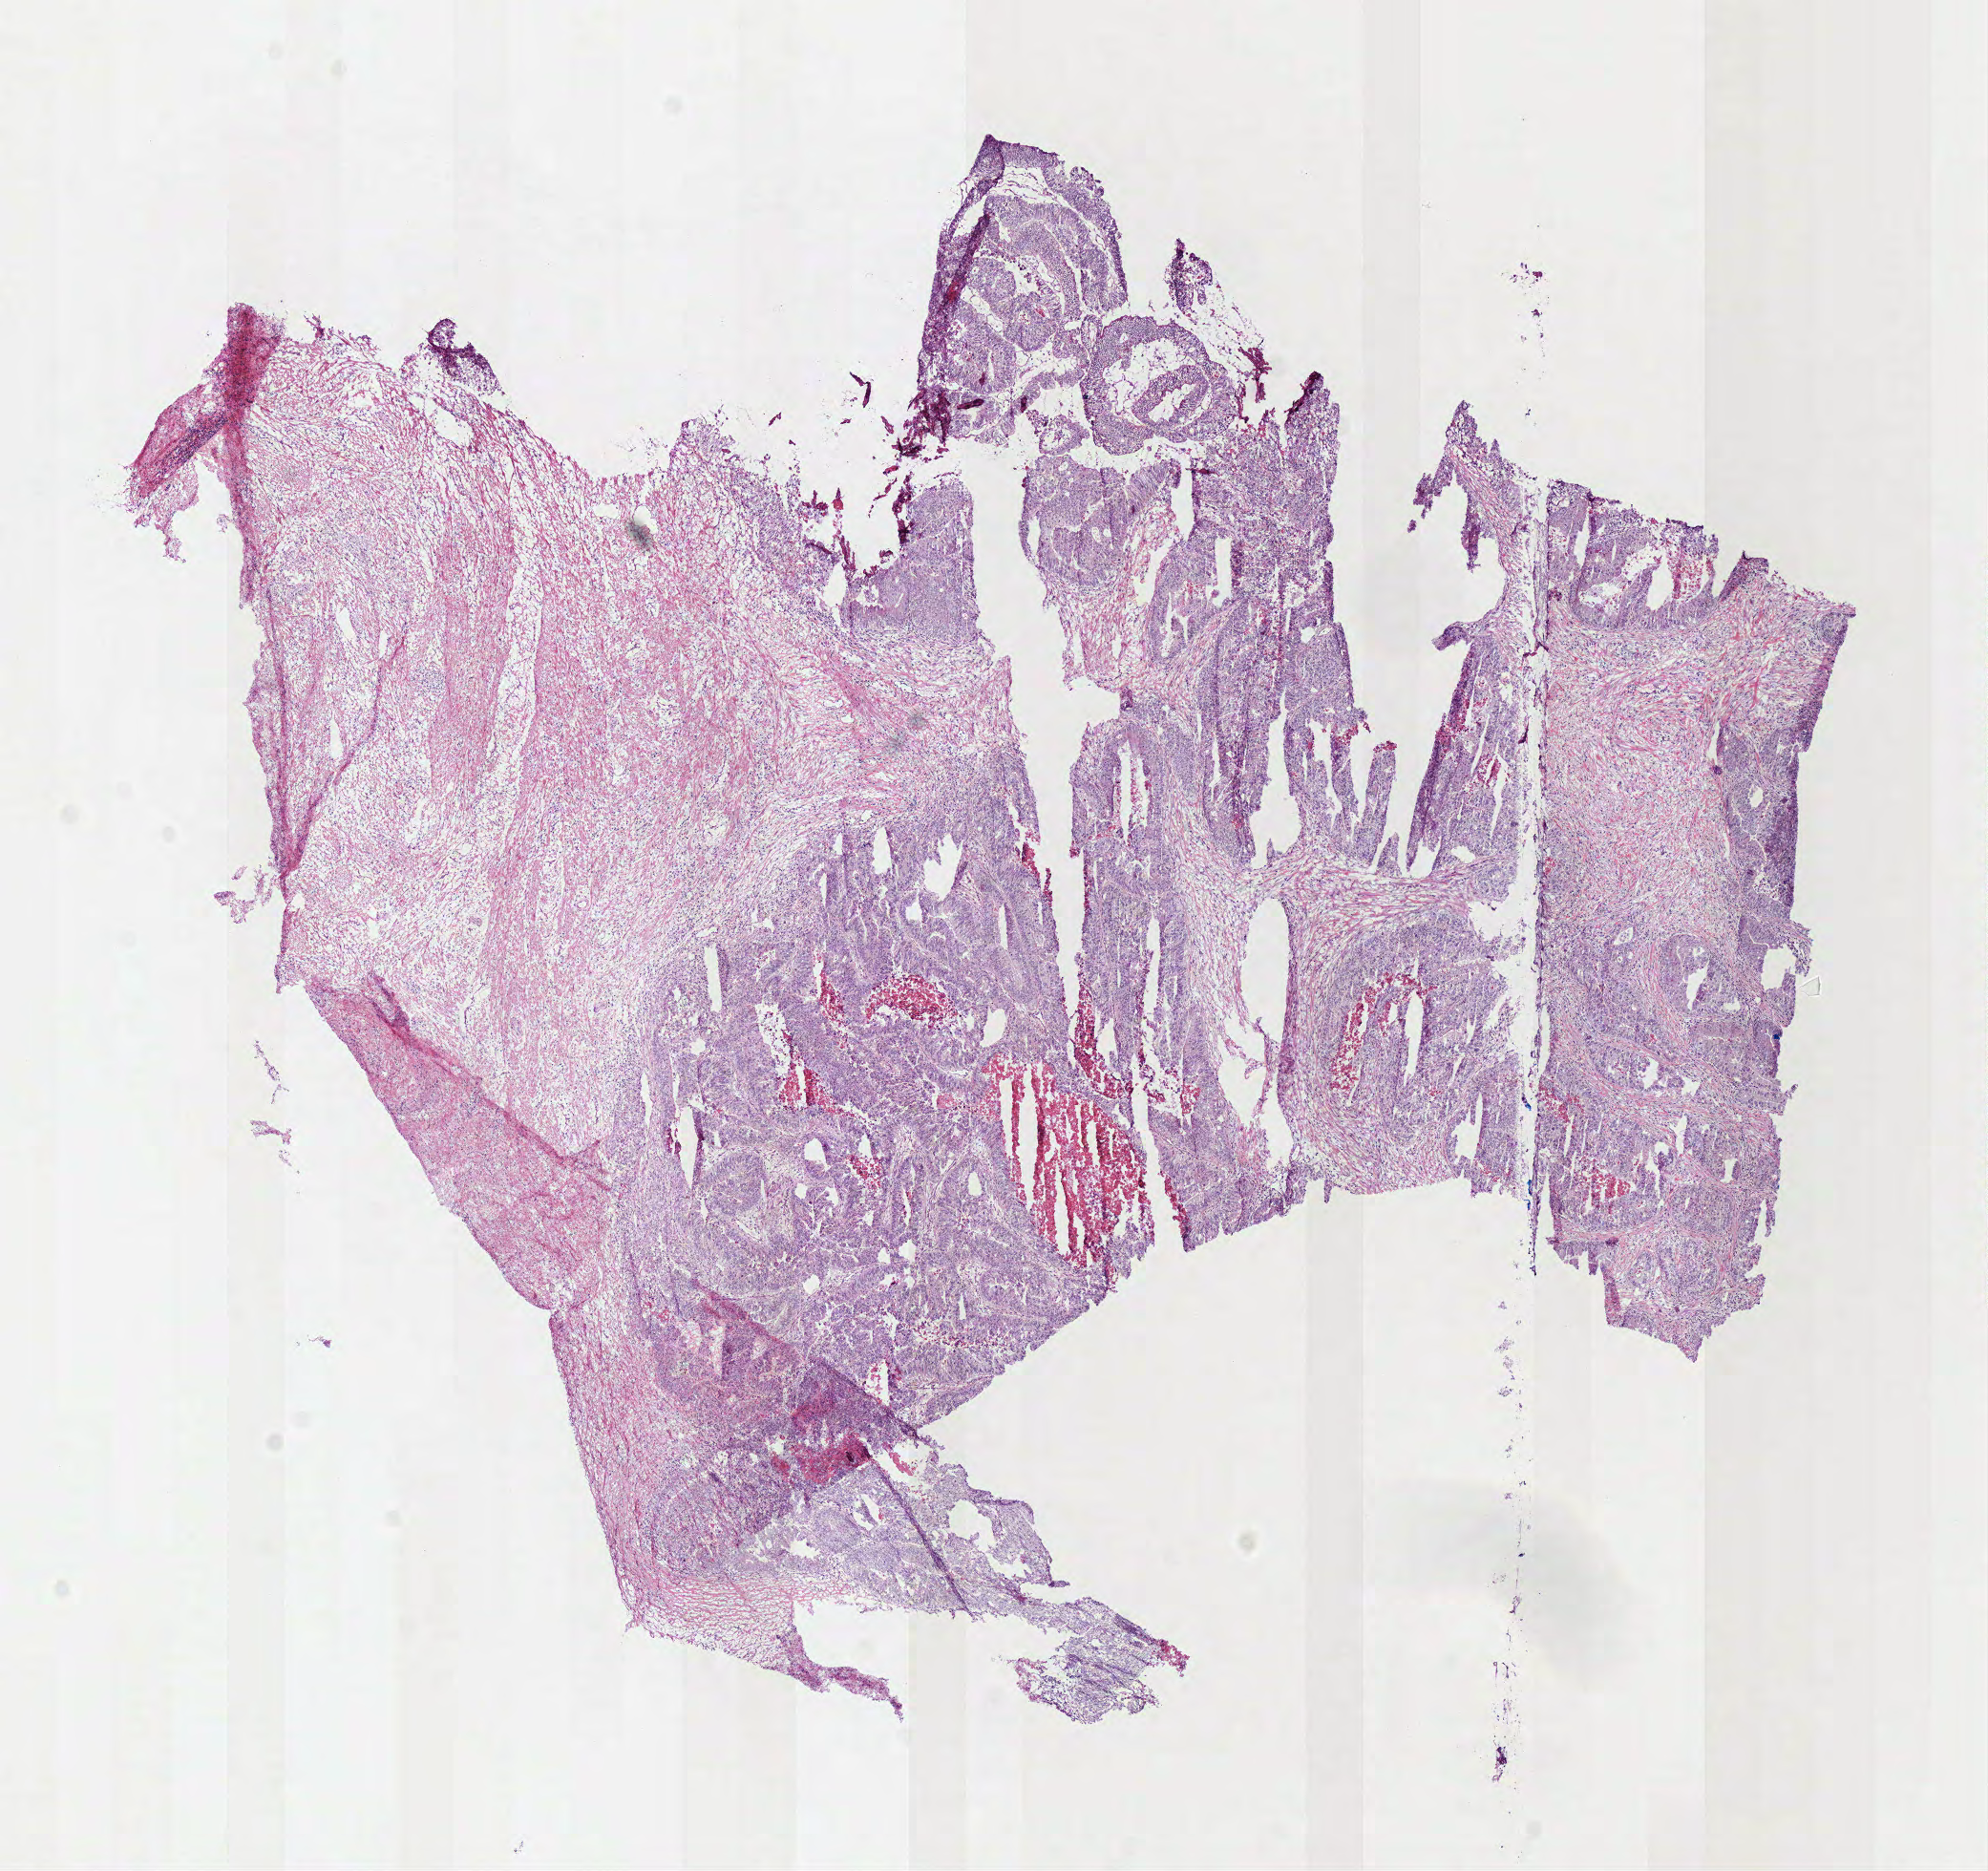
H&E-stained whole-slide image — low-resolution overview of the scanned area, about 8.2 x 7.7 mm (slide scanned at 40x), frozen section, sample: primary tumour, colon. Female patient; age at initial diagnosis 51 years. Composition of this section per pathologist review: tumour cells 52%, tumour nuclei 70%, normal cells 0%, stromal cells 40%, necrosis 8%.
- AJCC pathologic stage: I (7th edition)
- lymph nodes positive (case pathology): 0 of 8 examined
- pathologic diagnosis: Adenocarcinoma, NOS